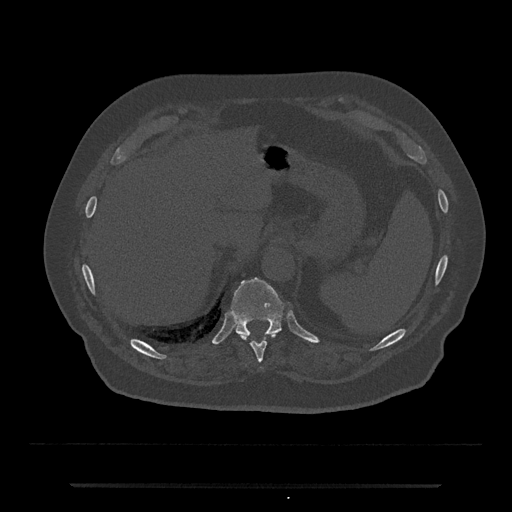
CT including the spine, one axial slice. Position 676 of 797 along the scan axis. Bone window (W 1800 / L 400 HU). 0.5 mm slice thickness. 512 × 512 image matrix, field of view 434 × 434 mm. Patient: male, 80 years. From the clinical record (not read from this slice): primary cancer: prostate; vertebrae with lytic lesions (as recorded): L1, T11.
Annotated regions visible in this slice (semi-automatic segmentation, software-assisted and operator-edited):
- T10 vertebra: bounding box <242,333,277,370> (left, top, right, bottom; pixels)
- T11 vertebra: <231,277,285,337>